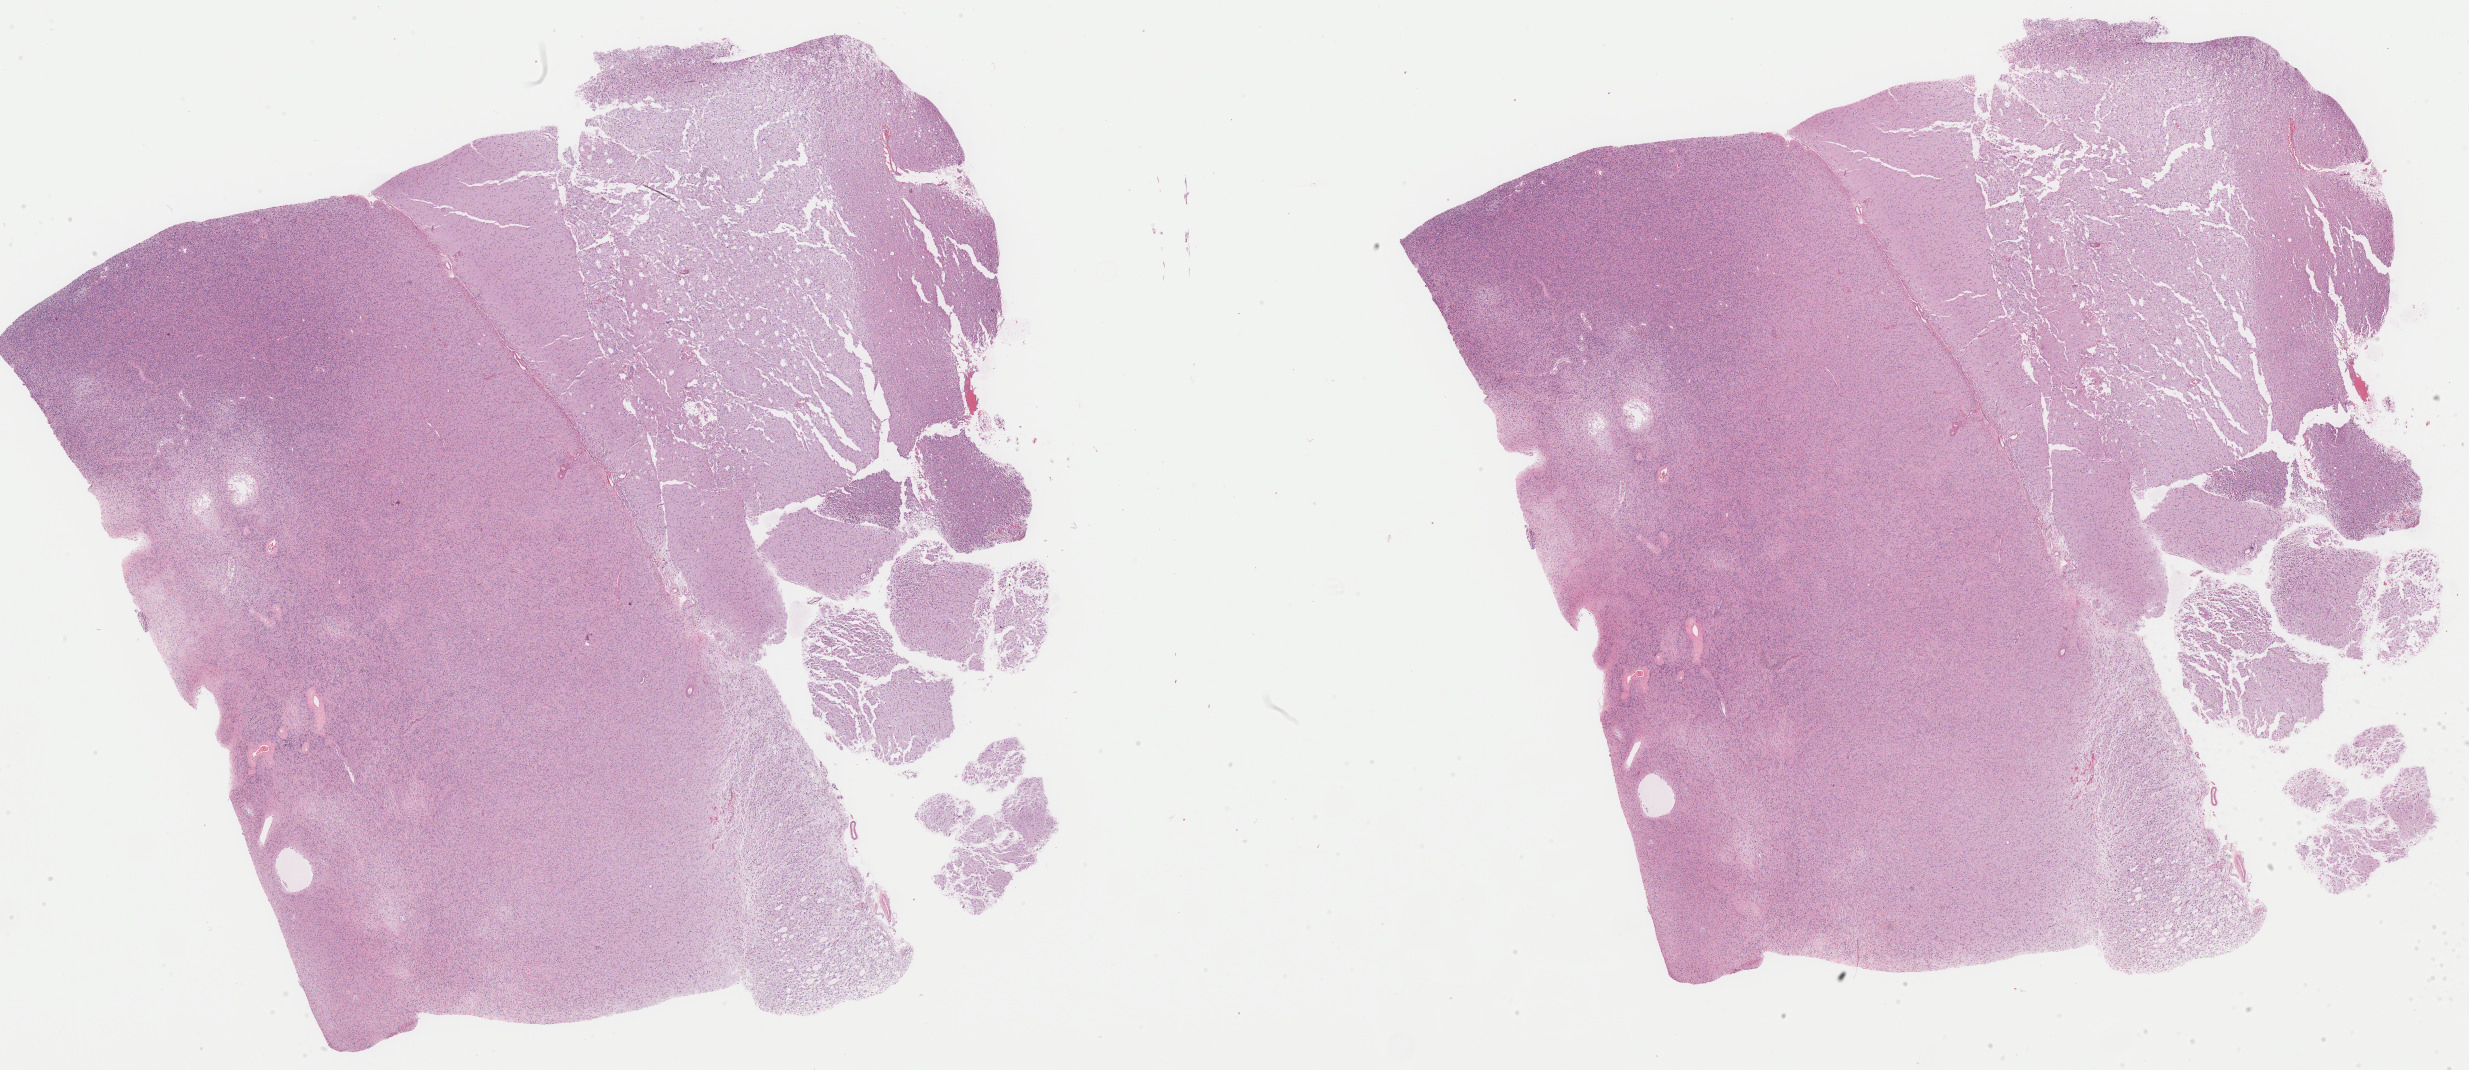
Whole-slide histology image, H&E, low-resolution overview of the scanned area, about 38.9 x 16.9 mm. Formalin-fixed paraffin-embedded (FFPE) diagnostic section. Primary tumour sample from the brain. Patient: female, age at initial diagnosis 41 years.
Pathologic diagnosis: Astrocytoma, anaplastic (frontal lobe).